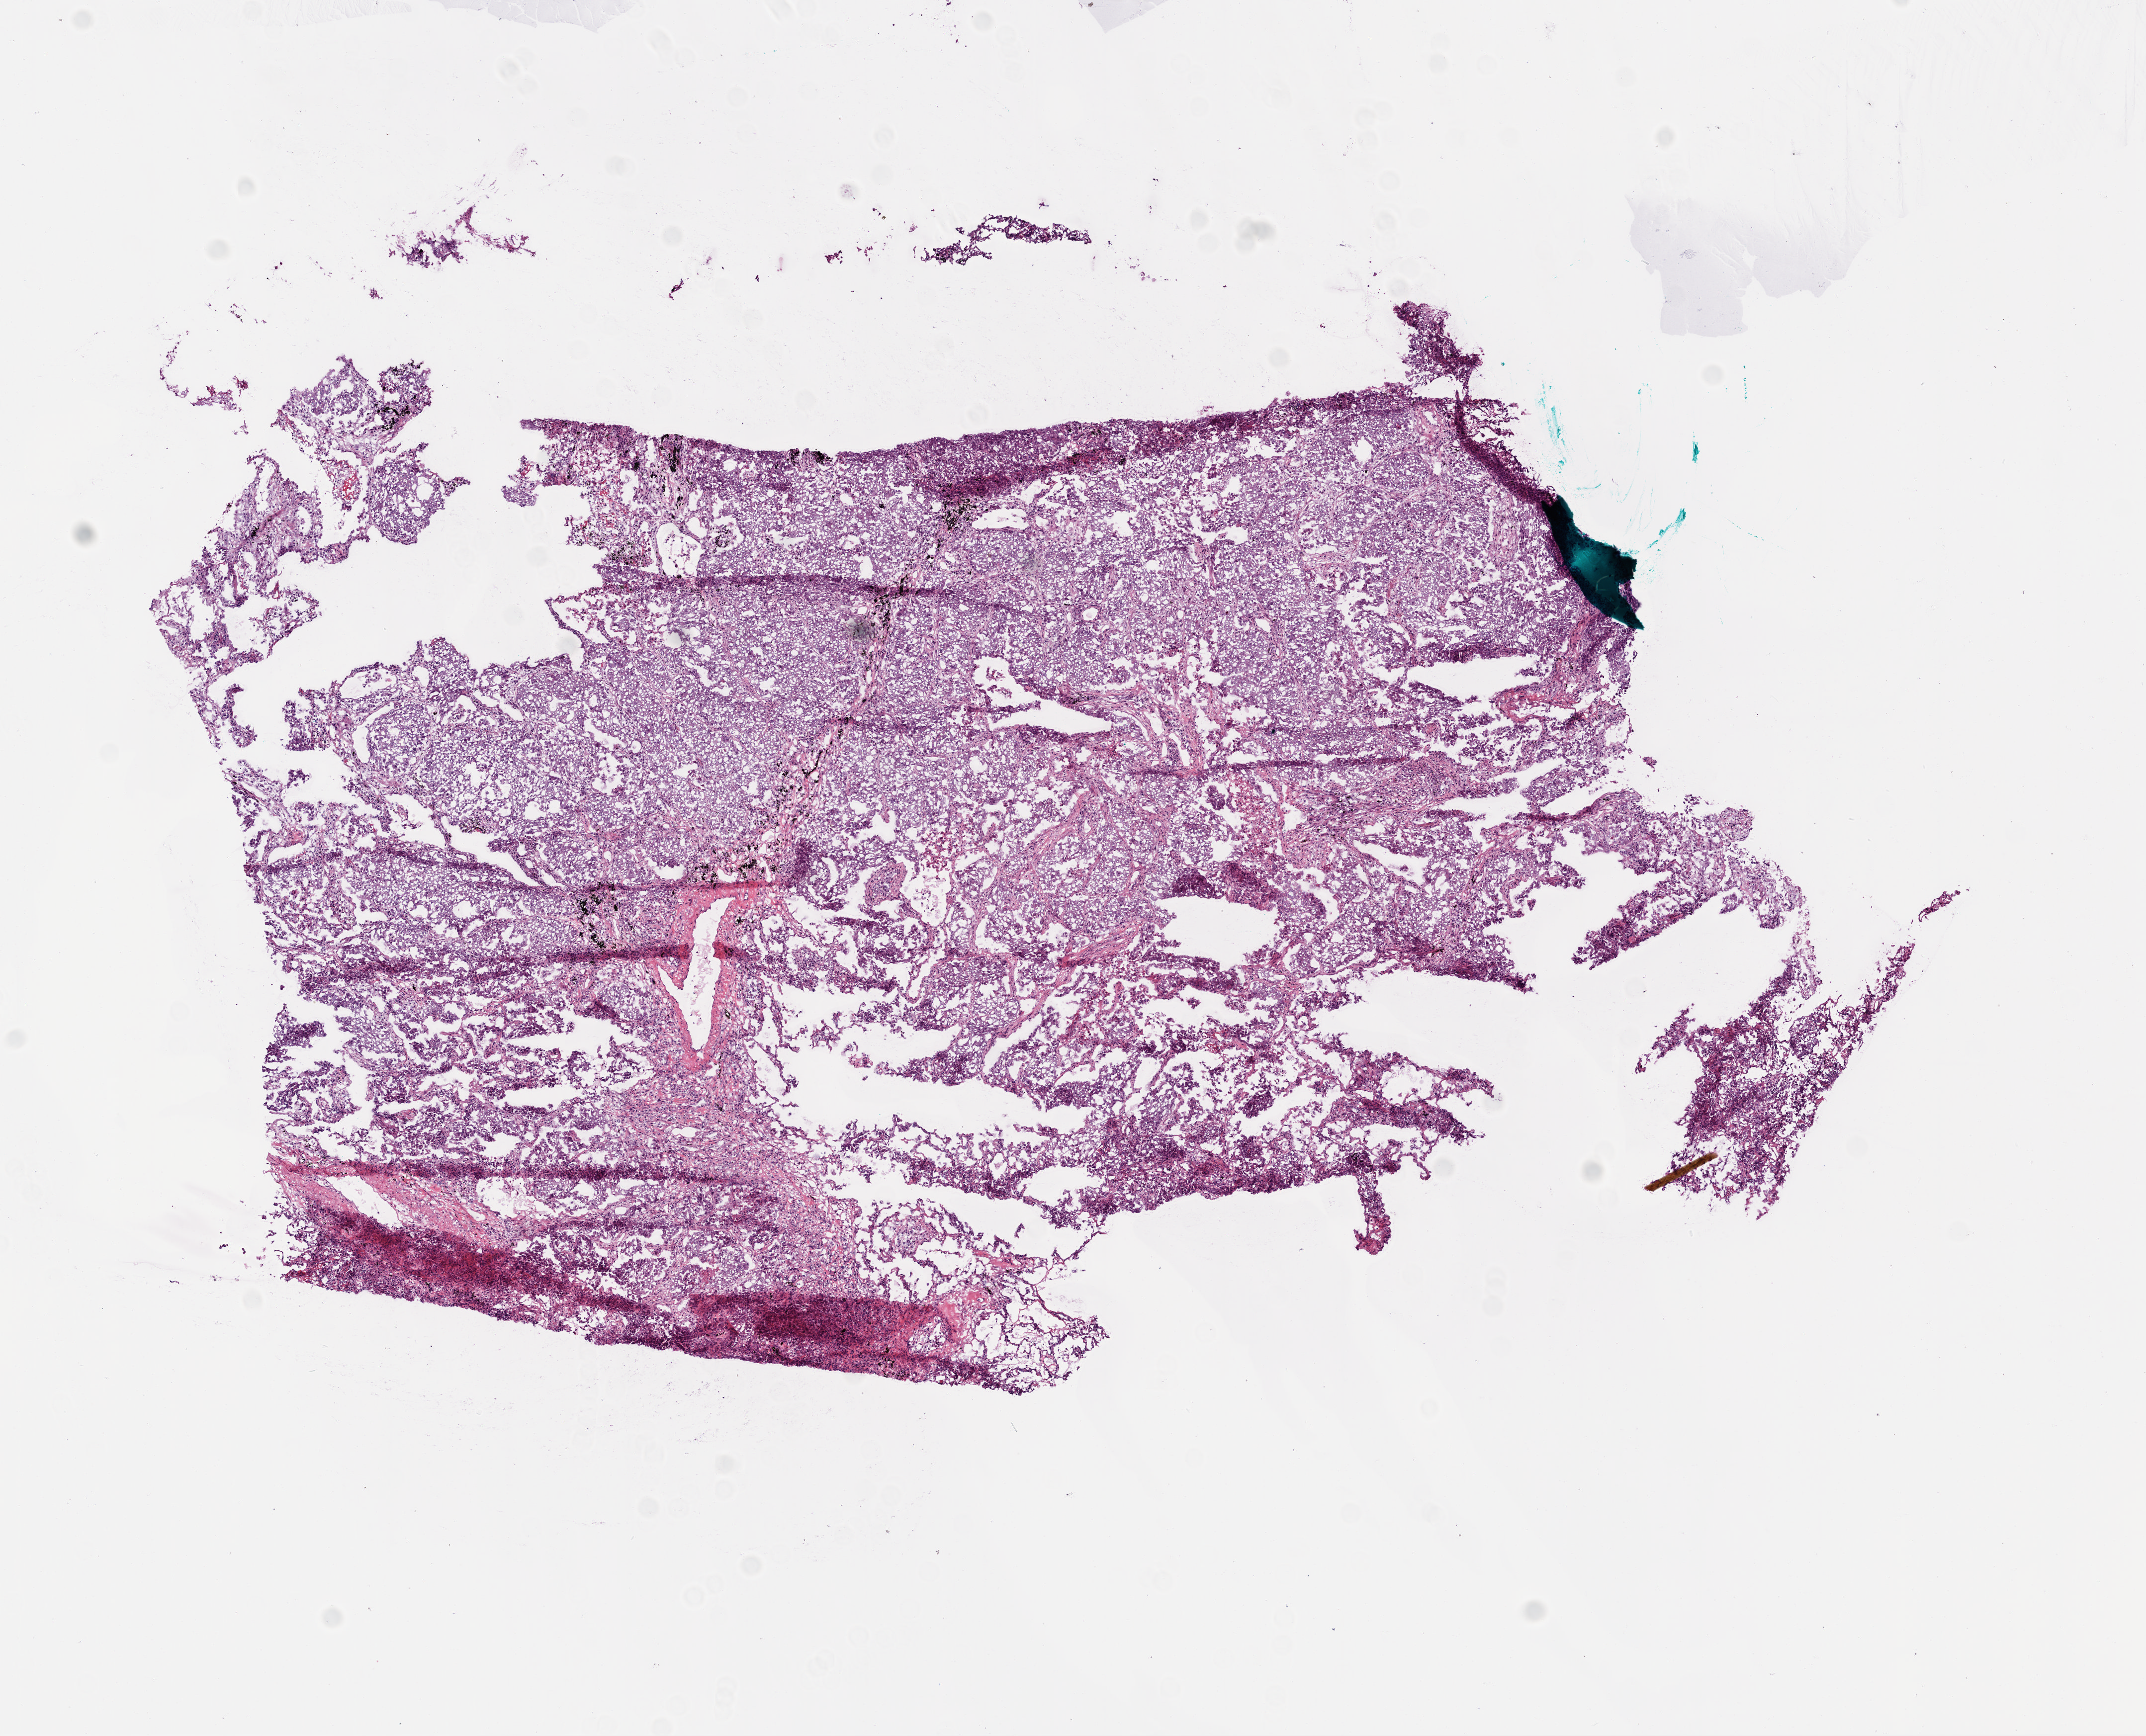
H&E-stained whole-slide image, low-resolution overview of the scanned area, about 8.7 x 7.0 mm (slide scanned at 20x); frozen section; primary tumour sample from the lung. Male patient; age at initial diagnosis 62 years.
Pathologic diagnosis: Squamous cell carcinoma, NOS.